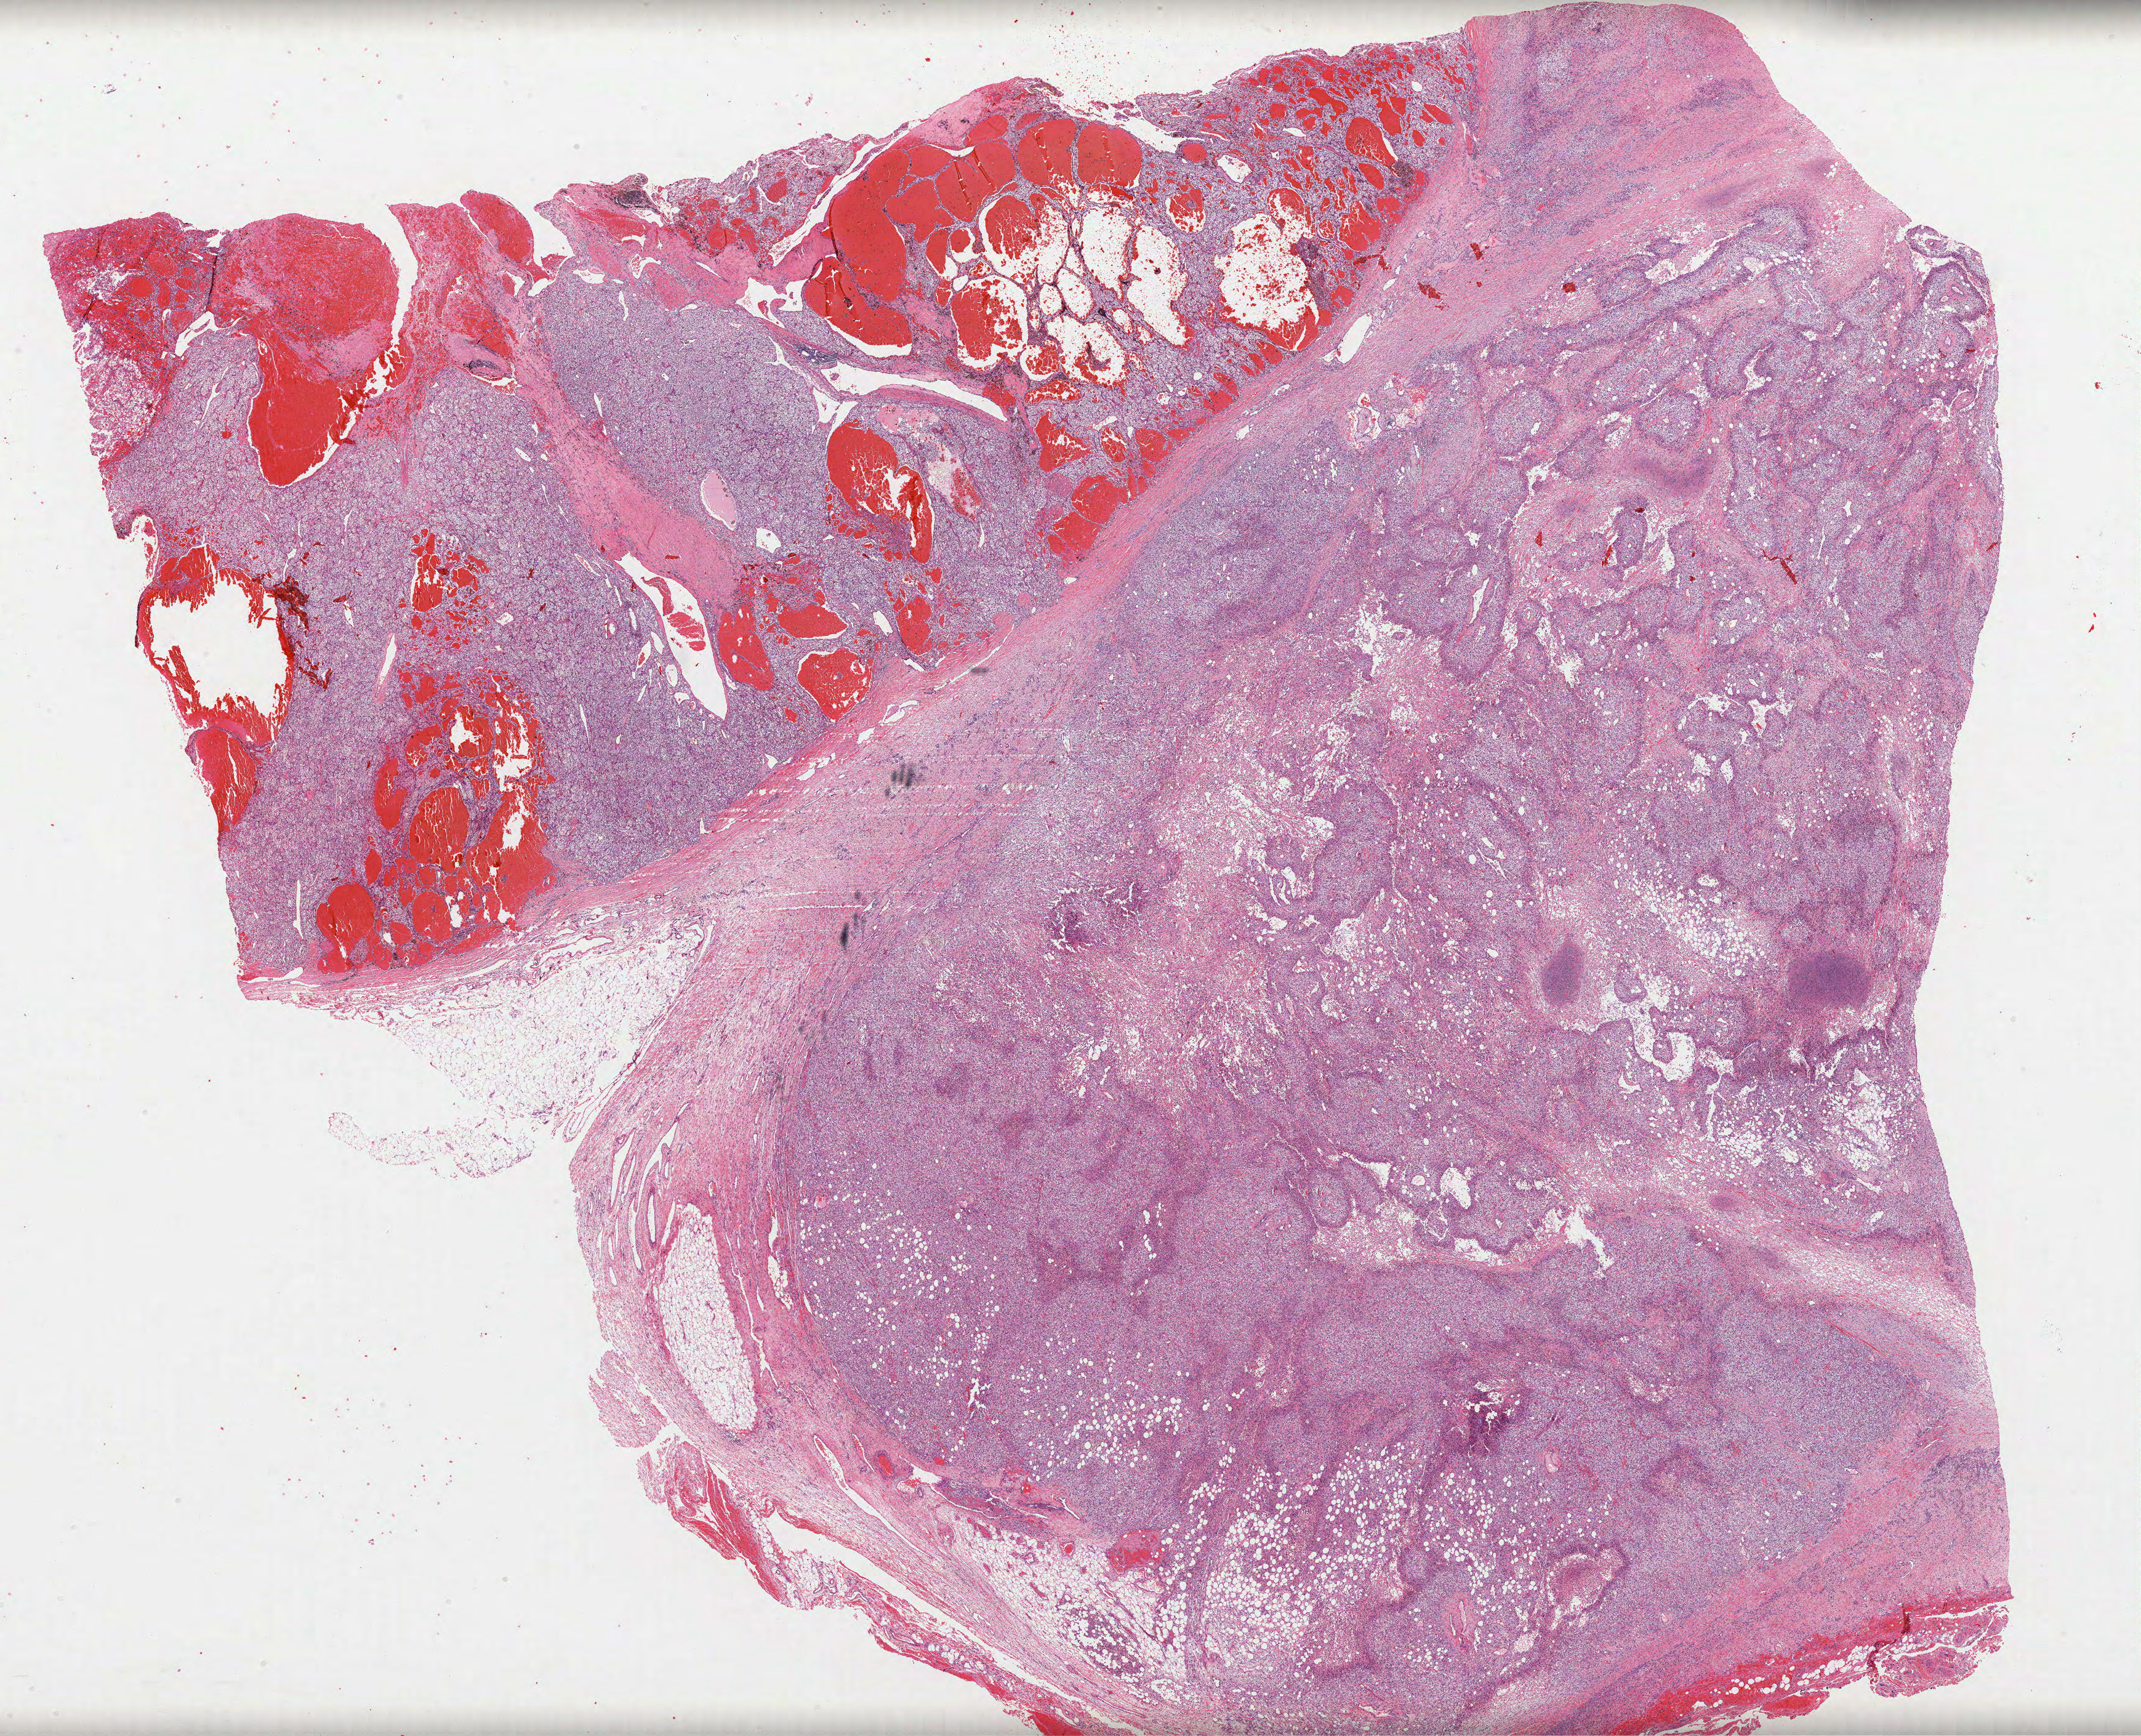
H&E-stained whole-slide image, shown as a low-resolution overview of the whole scanned area (about 28.0 x 22.7 mm, acquisition: 40x scan). Formalin-fixed paraffin-embedded (FFPE) diagnostic section. Primary tumour sample from the kidney. Female patient; age at initial diagnosis 86 years. Histologic grade: G4 (undifferentiated).
Diagnosis: Clear cell adenocarcinoma, NOS. AJCC pathologic stage: III.